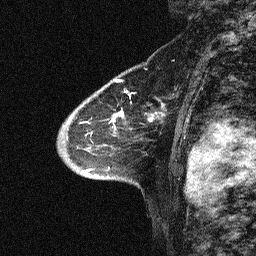
Breast MRI (dynamic contrast-enhanced), one sagittal slice; position 43 of 64 along the scan axis; dynamic contrast-enhanced study with each time point stored as its own series, time point 2 of 3 at this slice position (early post-contrast, ordered by acquisition time); 1.5 T; TE 4.5 ms, TR 11 ms; 2.06 mm slice thickness; 256 × 256 image matrix, field of view 200 × 200 mm. Patient: female, 46 years. Case-level facts recorded for this patient, not image findings: setting: breast cancer imaged before/during neoadjuvant chemotherapy; receptor status: HER2-positive.
Annotated regions visible in this slice (semi-automatic segmentation, software-assisted and operator-edited):
- analysis volume of interest (the breast-tissue region the enhancement analysis was run in; not a lesion): bounding box [x1, y1, x2, y2] px = [46, 51, 180, 169]
- tumour enhancement mask (voxels above the 90 % enhancement threshold inside the analysis volume of interest): [111, 110, 154, 121]